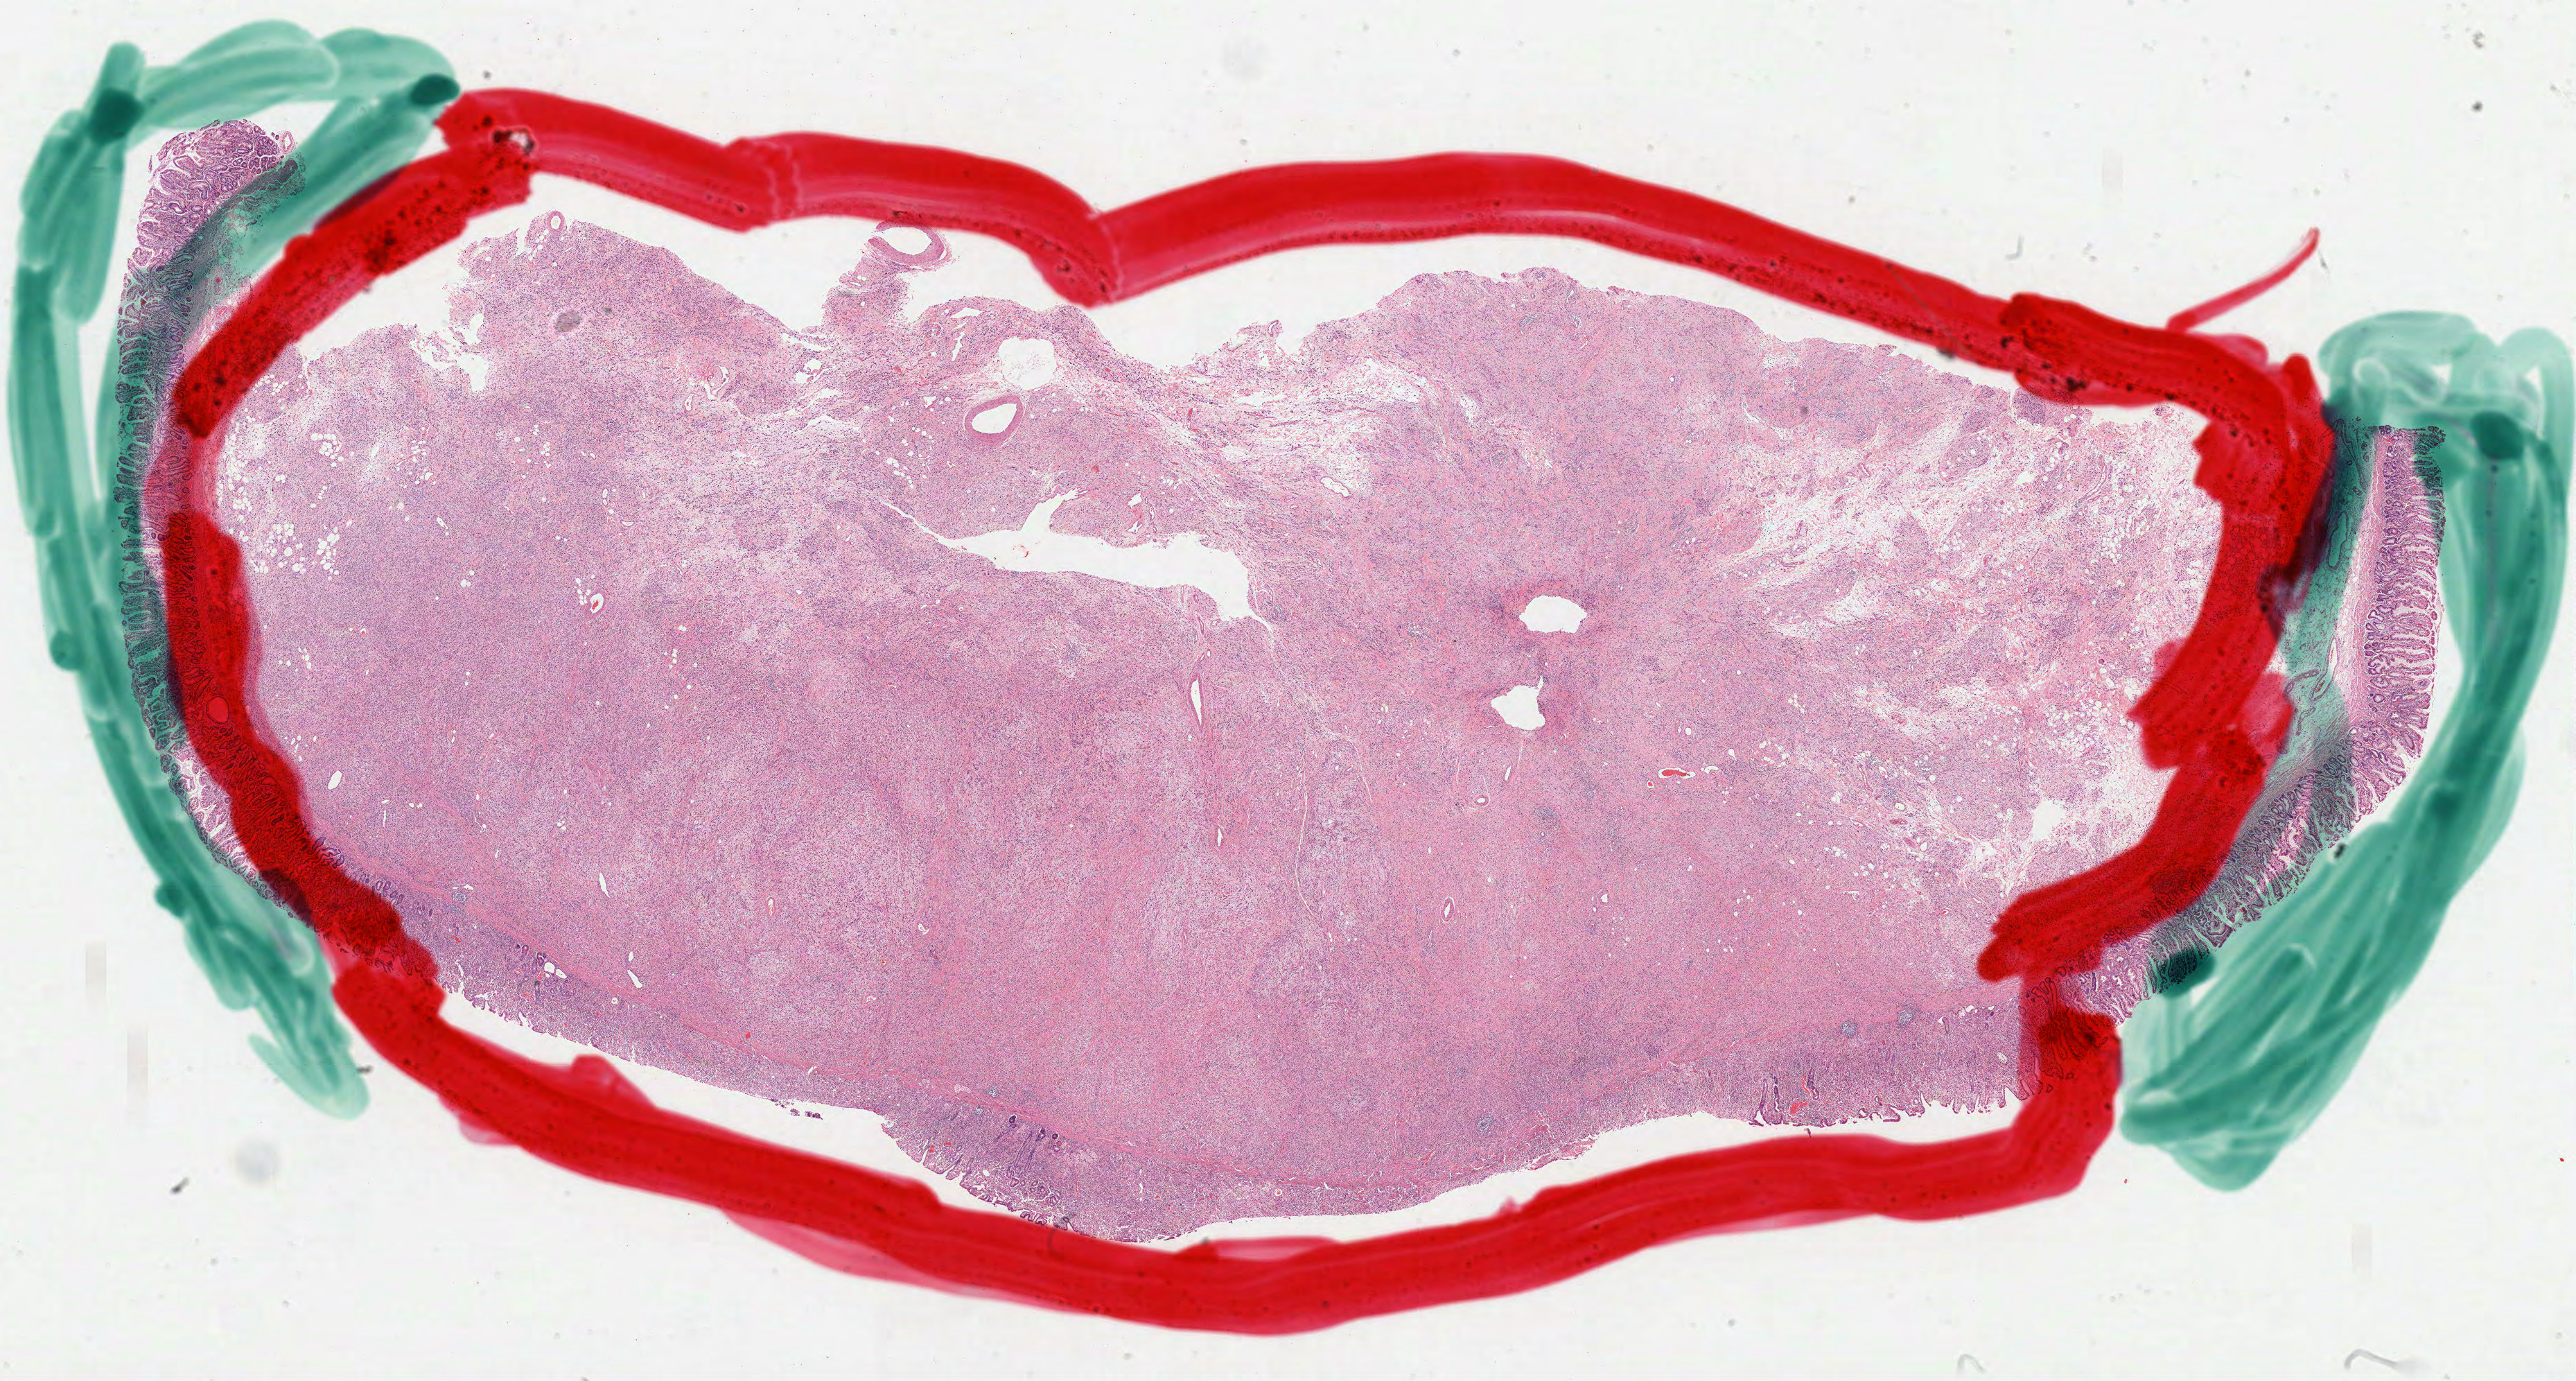
Whole-slide histology image, Hematoxylin and eosin (H&E) stained, a low-resolution overview of the entire scanned area, about 30.0 x 16.1 mm (slide scanned at 40x); formalin-fixed paraffin-embedded (FFPE) diagnostic section; stomach, primary tumour sample. Patient: male, age at initial diagnosis 61 years.
Histologic diagnosis: Carcinoma, diffuse type (gastric antrum).